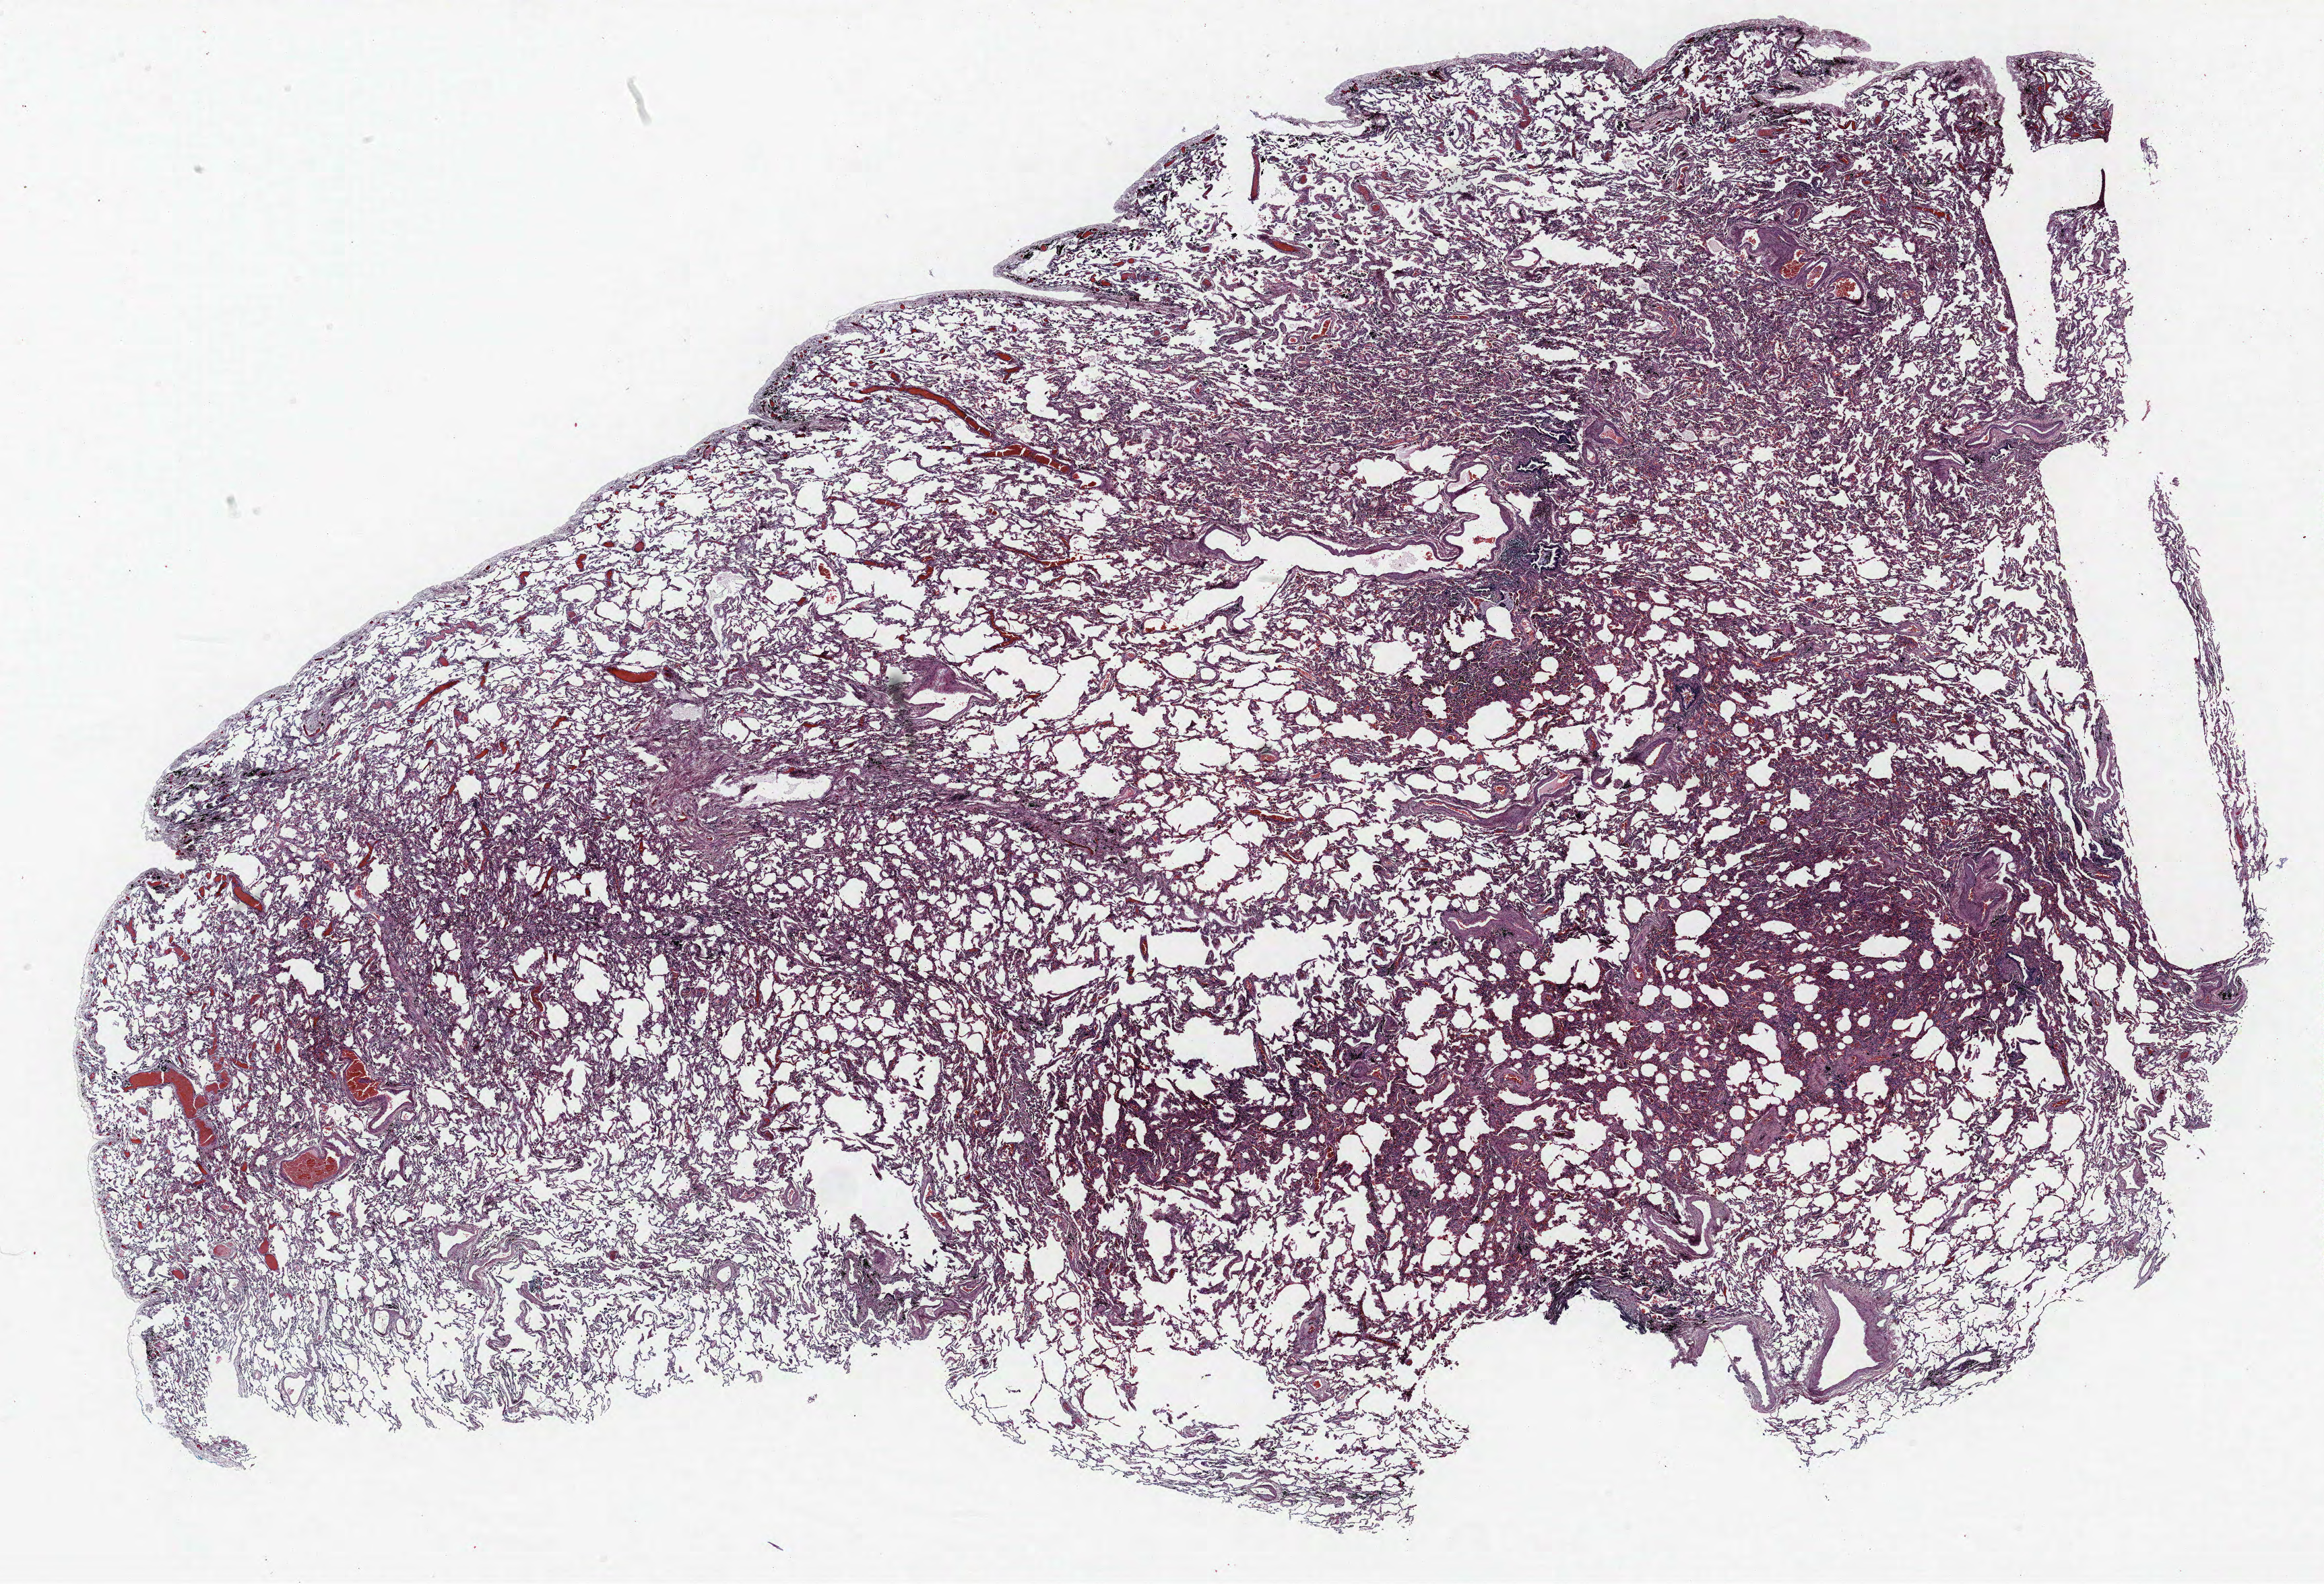
Whole-slide histology image, H&E, shown as a low-resolution overview of the whole scanned area (about 27.6 x 18.8 mm, acquisition: 40x scan); FFPE section; lung tissue. Female patient, aged 59 at enrolment. Grade: well differentiated (G1).
Stage (AJCC 6th edition): IA. Participant's lung-cancer diagnosis: Bronchiolo-alveolar adenocarcinoma, NOS (ICD-O-3 8250/3). ICD-O-3 topography: upper lobe of lung (C34.1). Primary tumour location (clinical record): right upper lobe. Tumour size (pathology): 4 mm.